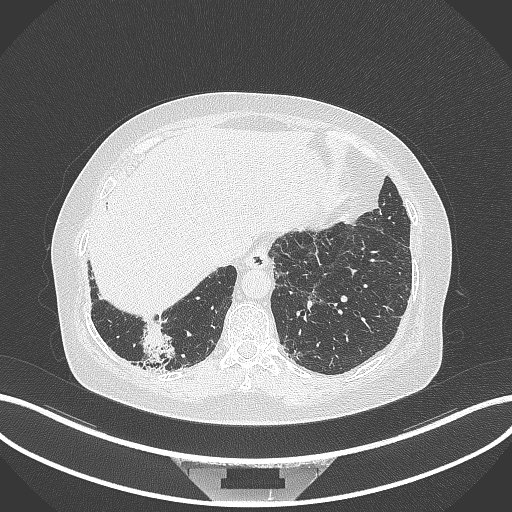
Chest CT, one axial slice. Slice 26 of 296 in the series (ordered by position). Reconstruction kernel B70f. Lung window (W 1500 / L -600 HU). 512 × 512 image matrix, field of view 400 × 400 mm. Patient: female, 65 years. Case-level facts recorded for this patient, not image findings: clinical TNM (as recorded): T2b N1 M0.
Annotated regions visible in this slice (bounding box drawn by a radiologist):
- lung tumour (recorded histology: adenocarcinoma): bounding box [x1, y1, x2, y2] px = [138, 319, 177, 367]